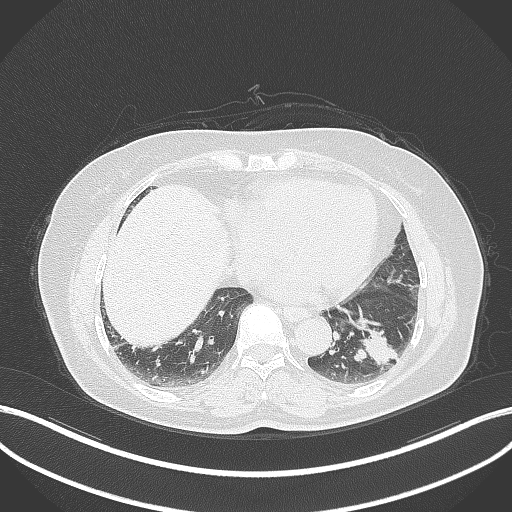
Chest CT, one axial slice. Slice 125 of 311 in the series (ordered by position). Reconstruction kernel B70f. Lung window (W 1500 / L -600 HU). 1 mm slice thickness. 512 × 512 image matrix. Female patient, age 59 years. Case-level facts recorded for this patient, not image findings: clinical TNM (as recorded): T2a N0 M0; histopathological grade: G2-3.
Structures marked on this image (bounding box drawn by a radiologist):
- lung tumour (recorded histology: adenocarcinoma): bounding box (x1, y1, x2, y2) in pixels: (351, 327, 401, 369)